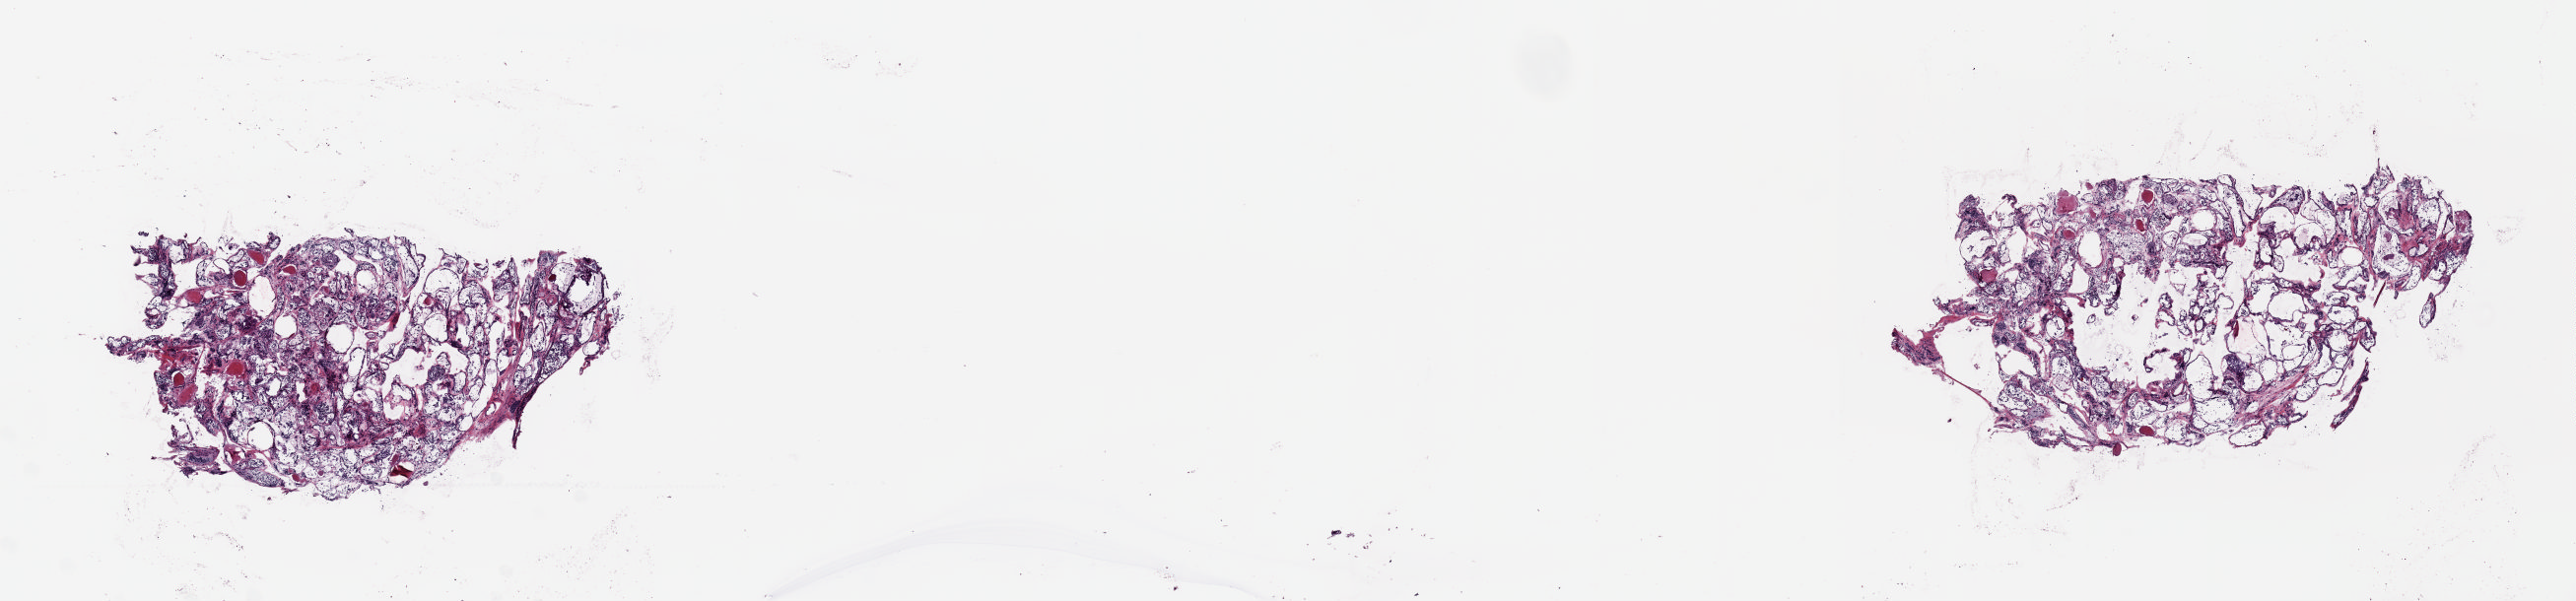
Digitized Hematoxylin and eosin (H&E) stained tissue section (whole slide) — shown as a low-resolution overview of the whole scanned area (about 20.6 x 4.8 mm, slide scanned at 20x). Frozen section. Solid tissue normal (non-tumour tissue) sample from the thyroid. Female, age 46 years at initial diagnosis. Slide review estimates, as recorded: tumour cells 0%, tumour nuclei 0%, normal cells 100%, stromal cells 0%, necrosis 0%. Infiltration values recorded for this section: lymphocyte infiltration 0%, monocyte infiltration 0%, neutrophil infiltration 0%.
• this section: solid tissue normal (non-tumour) sample from the same patient
• patient diagnosis: Papillary adenocarcinoma, NOS